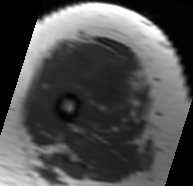
MRI of an extremity soft-tissue mass, one axial slice; slice 27 of 91 in the series (ordered by position); MR volume resampled by the dataset authors to the PET/CT grid (not the native acquisition matrix); 3.27 mm slice thickness; 193 × 186 image matrix. Female patient. From the clinical record (not read from this slice): histological type: malignant solitary fibrous tumor; grade: intermediate; site of the primary tumour: right thigh.
Annotated regions visible in this slice (expert contour drawn on MRI and transferred to this co-registered scan by the dataset authors):
- gross tumour volume including surrounding oedema: bounding box <44,37,146,118> (left, top, right, bottom; pixels)
- gross tumour volume (mass): <47,42,137,109>